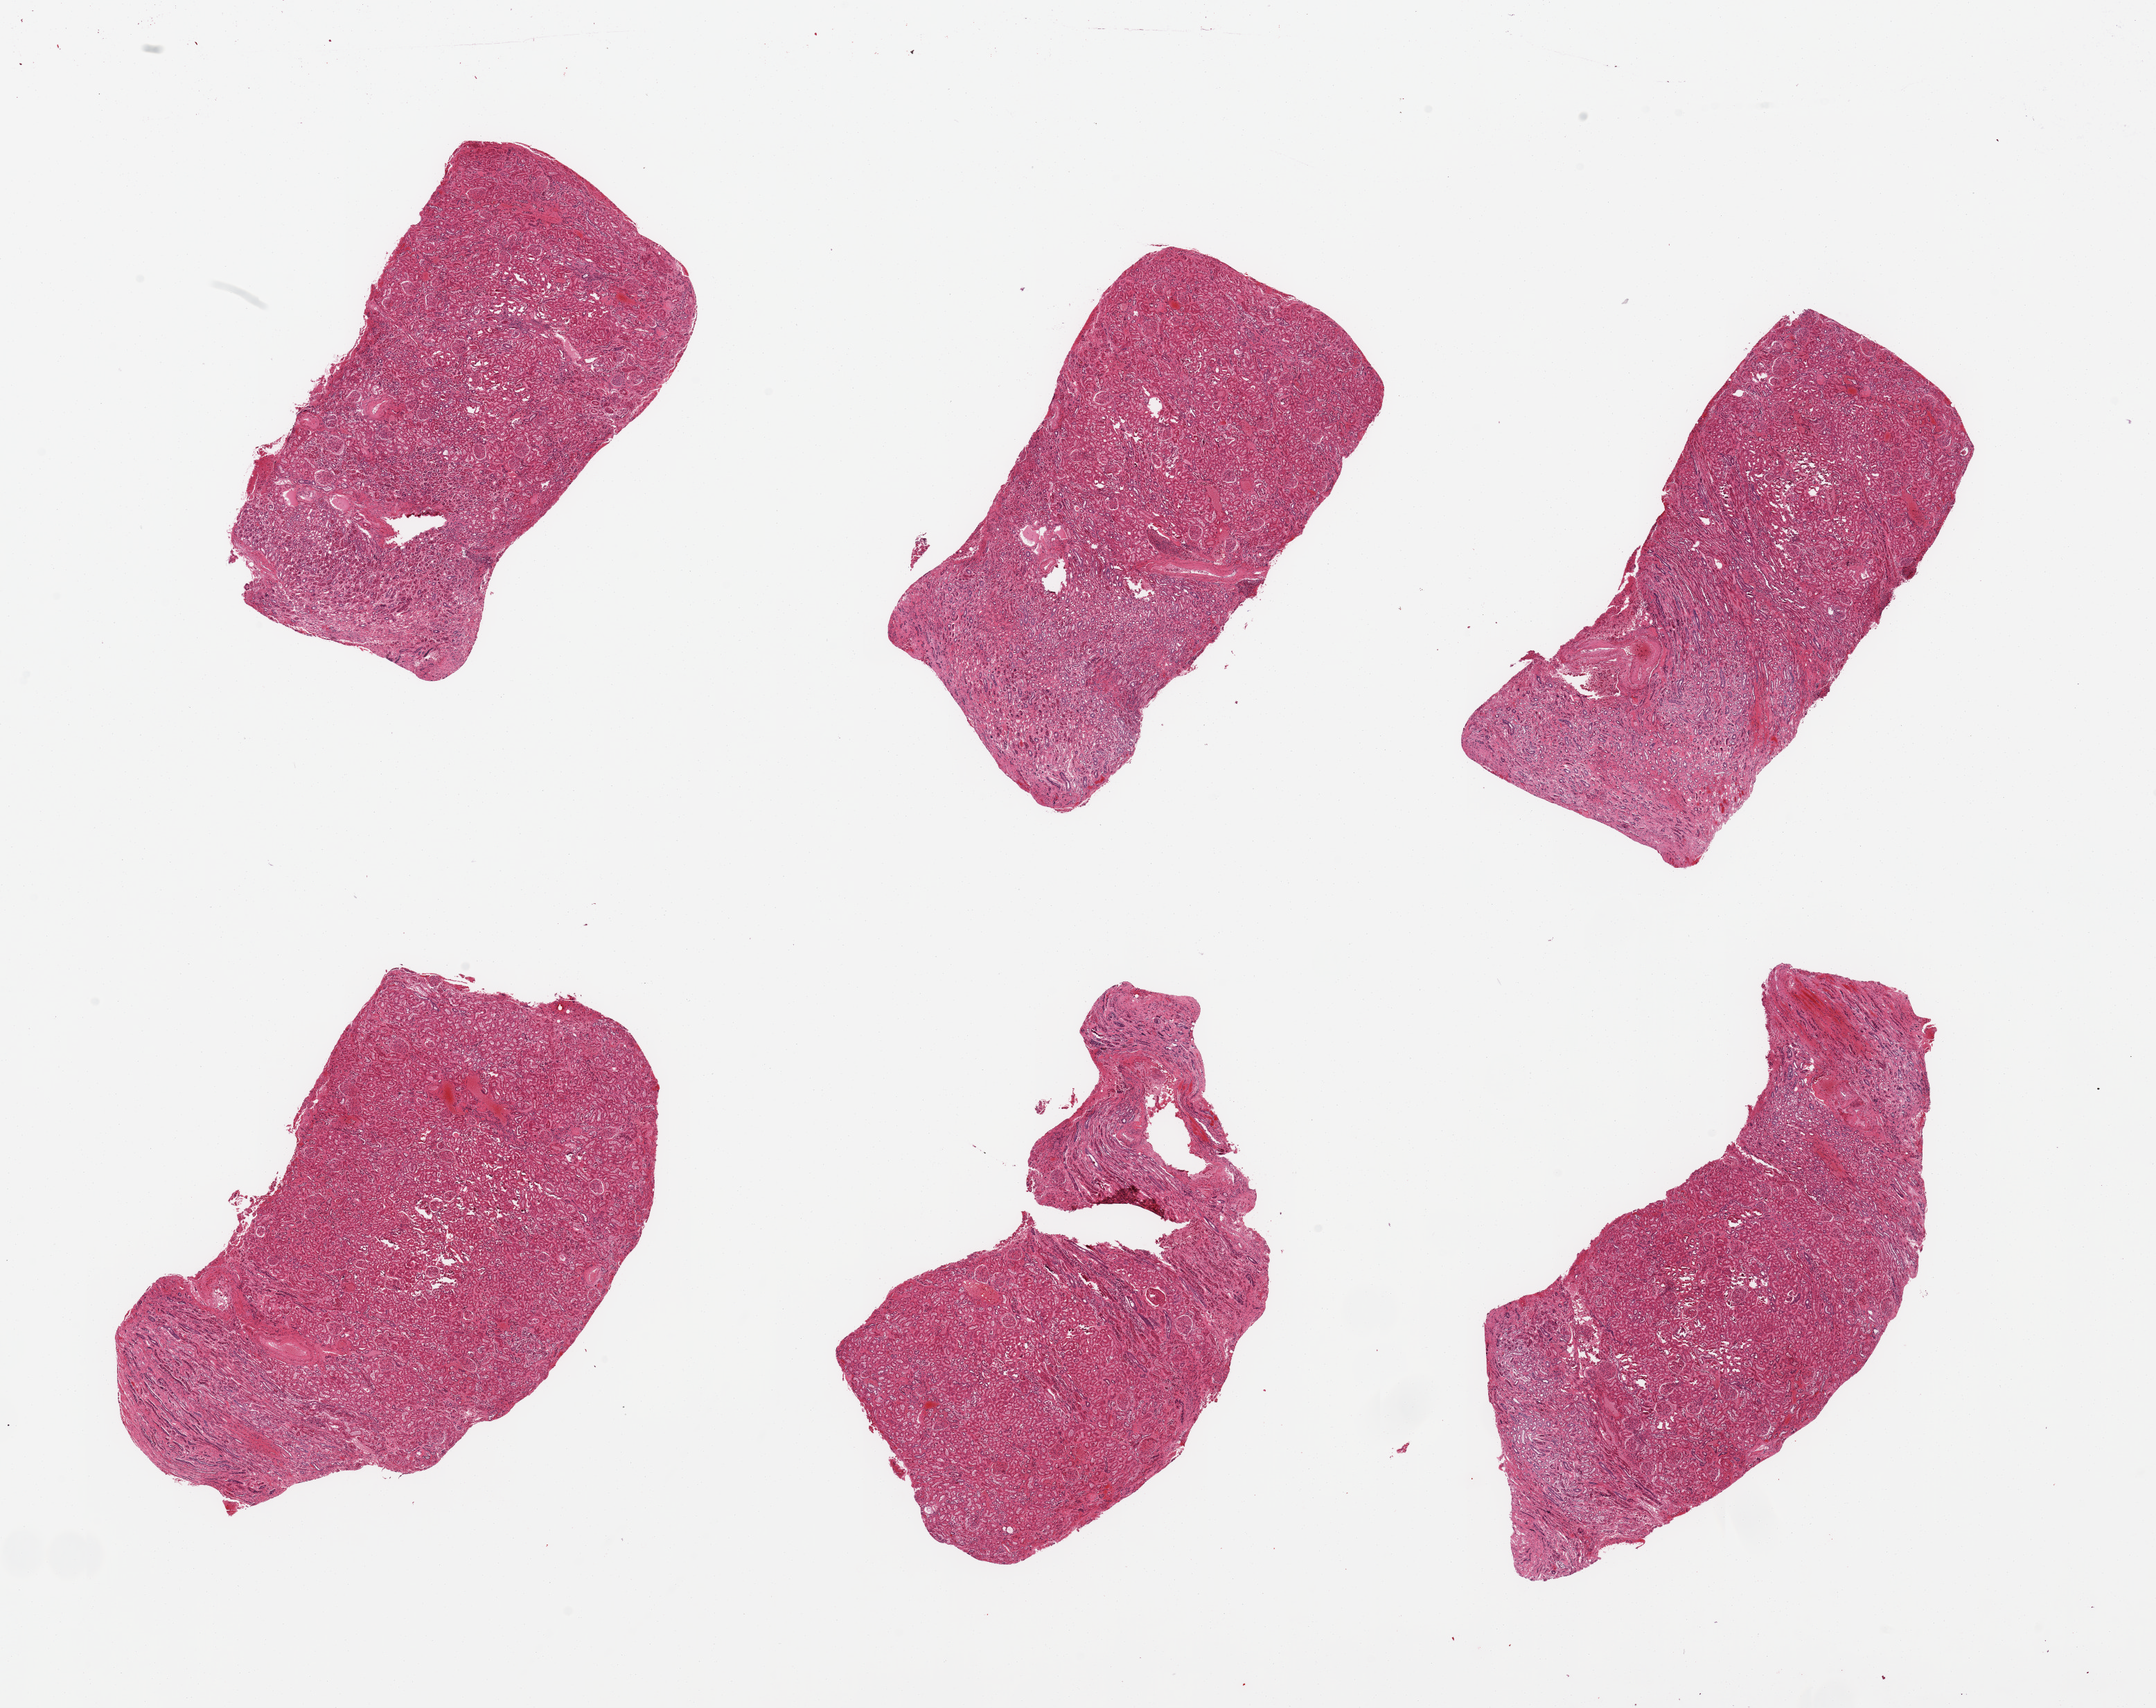
Whole-slide image, hematoxylin and eosin (H&E) stain, a low-resolution overview of the entire scanned area, about 24.6 x 19.5 mm; PAXgene-fixed, paraffin-embedded tissue; sampled site (target tissue): renal cortex; tissue donor sample.
Pathologist's review note for this sample: 6 pieces, glomeruli present.